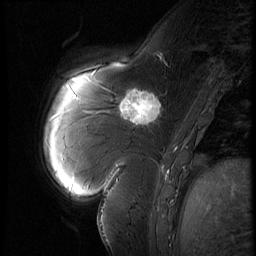
Breast MRI (dynamic contrast-enhanced), one sagittal slice; position 18 of 60 along the scan axis; 3 images stored at this slice position (order not interpretable as contrast timing); 1.5 T; TE 4.2 ms, TR 9 ms; 2.5 mm slice thickness; 256 × 256 image matrix, field of view 180 × 180 mm. Female patient, age 57 years. From the clinical record (not read from this slice): setting: breast cancer imaged before/during neoadjuvant chemotherapy; receptor status: triple-negative.
Outlined on this slice (semi-automatically segmented with operator editing):
- analysis volume of interest (the breast-tissue region the enhancement analysis was run in; not a lesion): bounding box (x1, y1, x2, y2) in pixels: (114, 83, 170, 131)
- tumour enhancement mask (voxels above the 140 % enhancement threshold inside the analysis volume of interest): (119, 92, 161, 125)